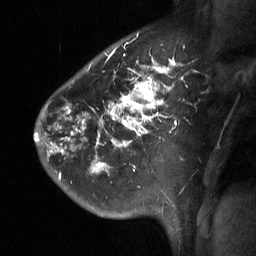
Breast MRI (dynamic contrast-enhanced), one sagittal slice. Slice 48 of 64 in the series (ordered by position). Dynamic contrast-enhanced study with each time point stored as its own series, time point 2 of 3 at this slice position (early post-contrast, ordered by acquisition time). 1.5 T. TE 4.8 ms, TR 27 ms. 2 mm slice thickness. 256 × 256 image matrix, field of view 200 × 200 mm. Patient: female, 42 years. Case-level facts recorded for this patient, not image findings: setting: breast cancer imaged before/during neoadjuvant chemotherapy; receptor status: triple-negative.
Outlined on this slice (semi-automatic segmentation, software-assisted and operator-edited):
- analysis volume of interest (the breast-tissue region the enhancement analysis was run in; not a lesion): bounding box [x1, y1, x2, y2] px = [49, 45, 199, 197]
- tumour enhancement mask (voxels above the 90 % enhancement threshold inside the analysis volume of interest): [50, 54, 177, 174]